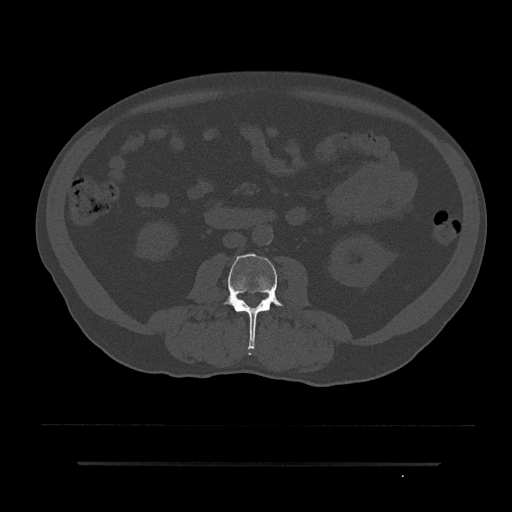
CT including the spine, one axial slice. Slice 3 of 797 in the series (ordered by position). 120 kVp. Bone window (W 1800 / L 400 HU). 0.5 mm slice thickness. 512 × 512 image matrix. Patient: male, 59 years. From the clinical record (not read from this slice): primary cancer: bile ducts; vertebrae with lytic lesions (as recorded): T10.
Outlined on this slice (semi-automatically segmented with operator editing):
- L3 vertebra: box from (x=222, y=253) to (x=288, y=349) px